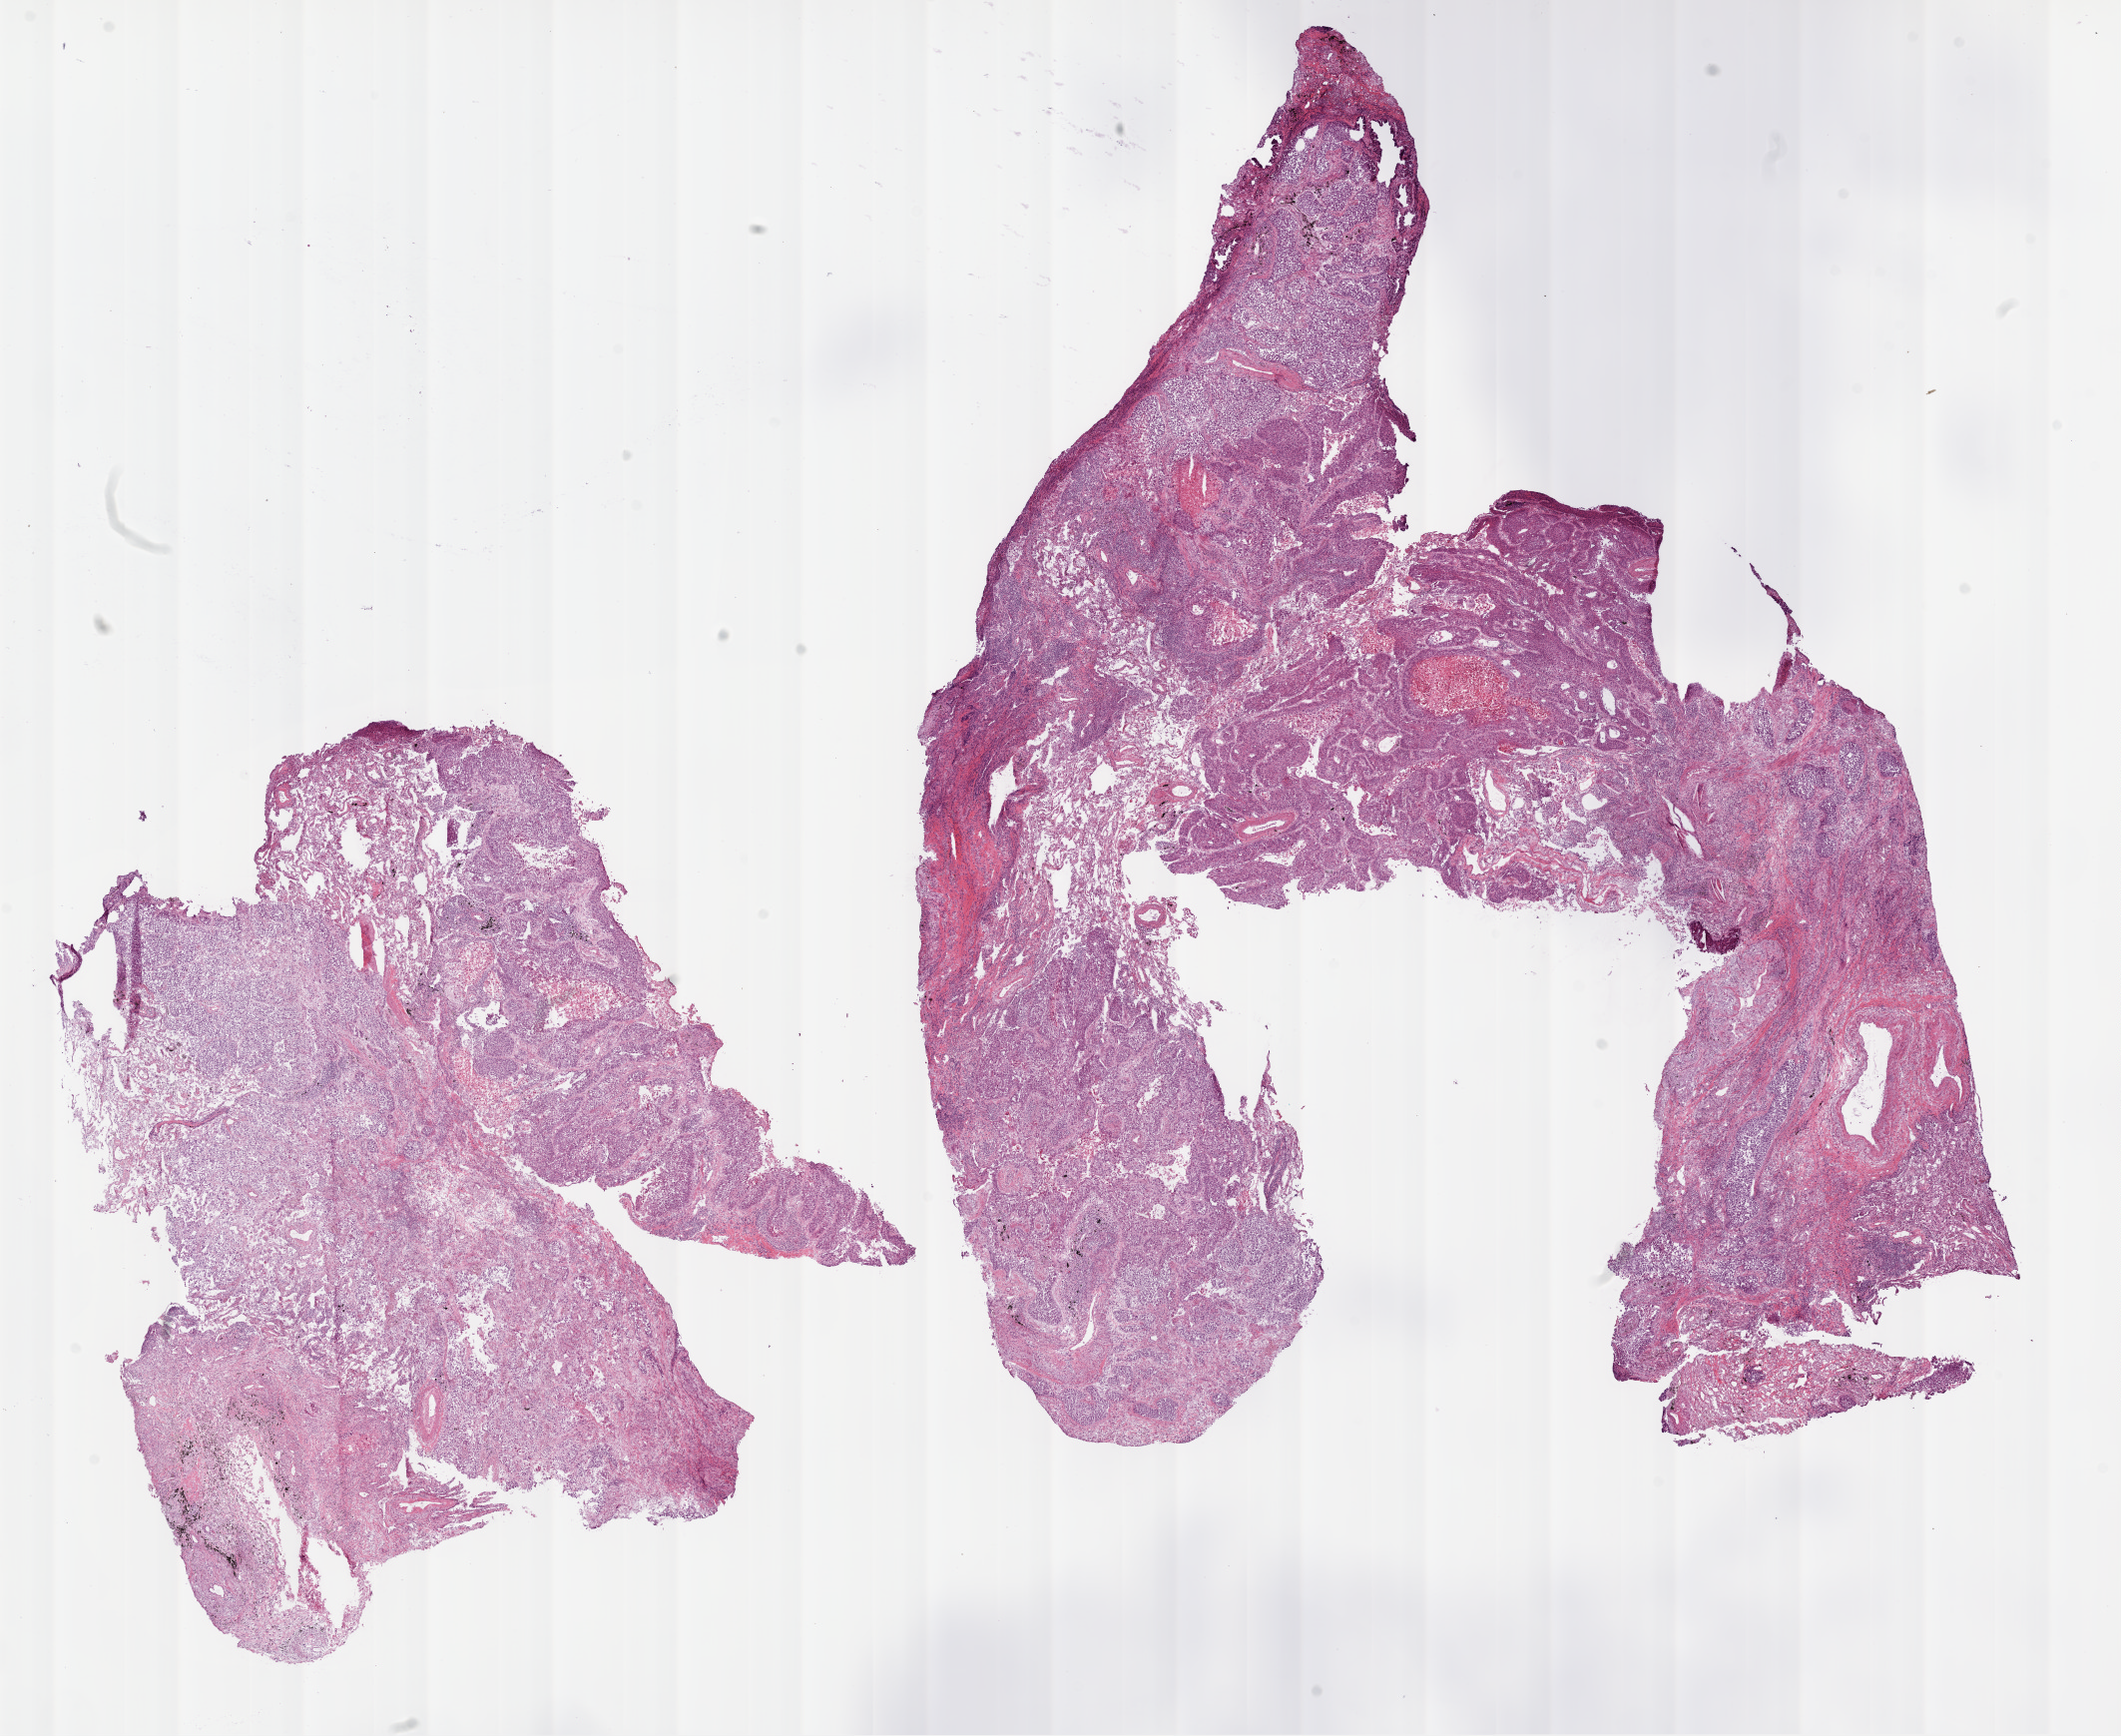
Whole-slide histology image, H&E, a low-resolution overview of the entire scanned area, about 17.1 x 14.0 mm (acquisition: 20x scan), frozen section, lung, primary tumour sample. Male, age 73 years at initial diagnosis. Pathologist review of this section (percent, as recorded): tumour cells 65%, tumour nuclei 75%, normal cells 10%, stromal cells 15%, necrosis 10%.
Laterality: left. Diagnosis: Squamous cell carcinoma, NOS (upper lobe, lung). AJCC pathologic stage: IB (6th edition).